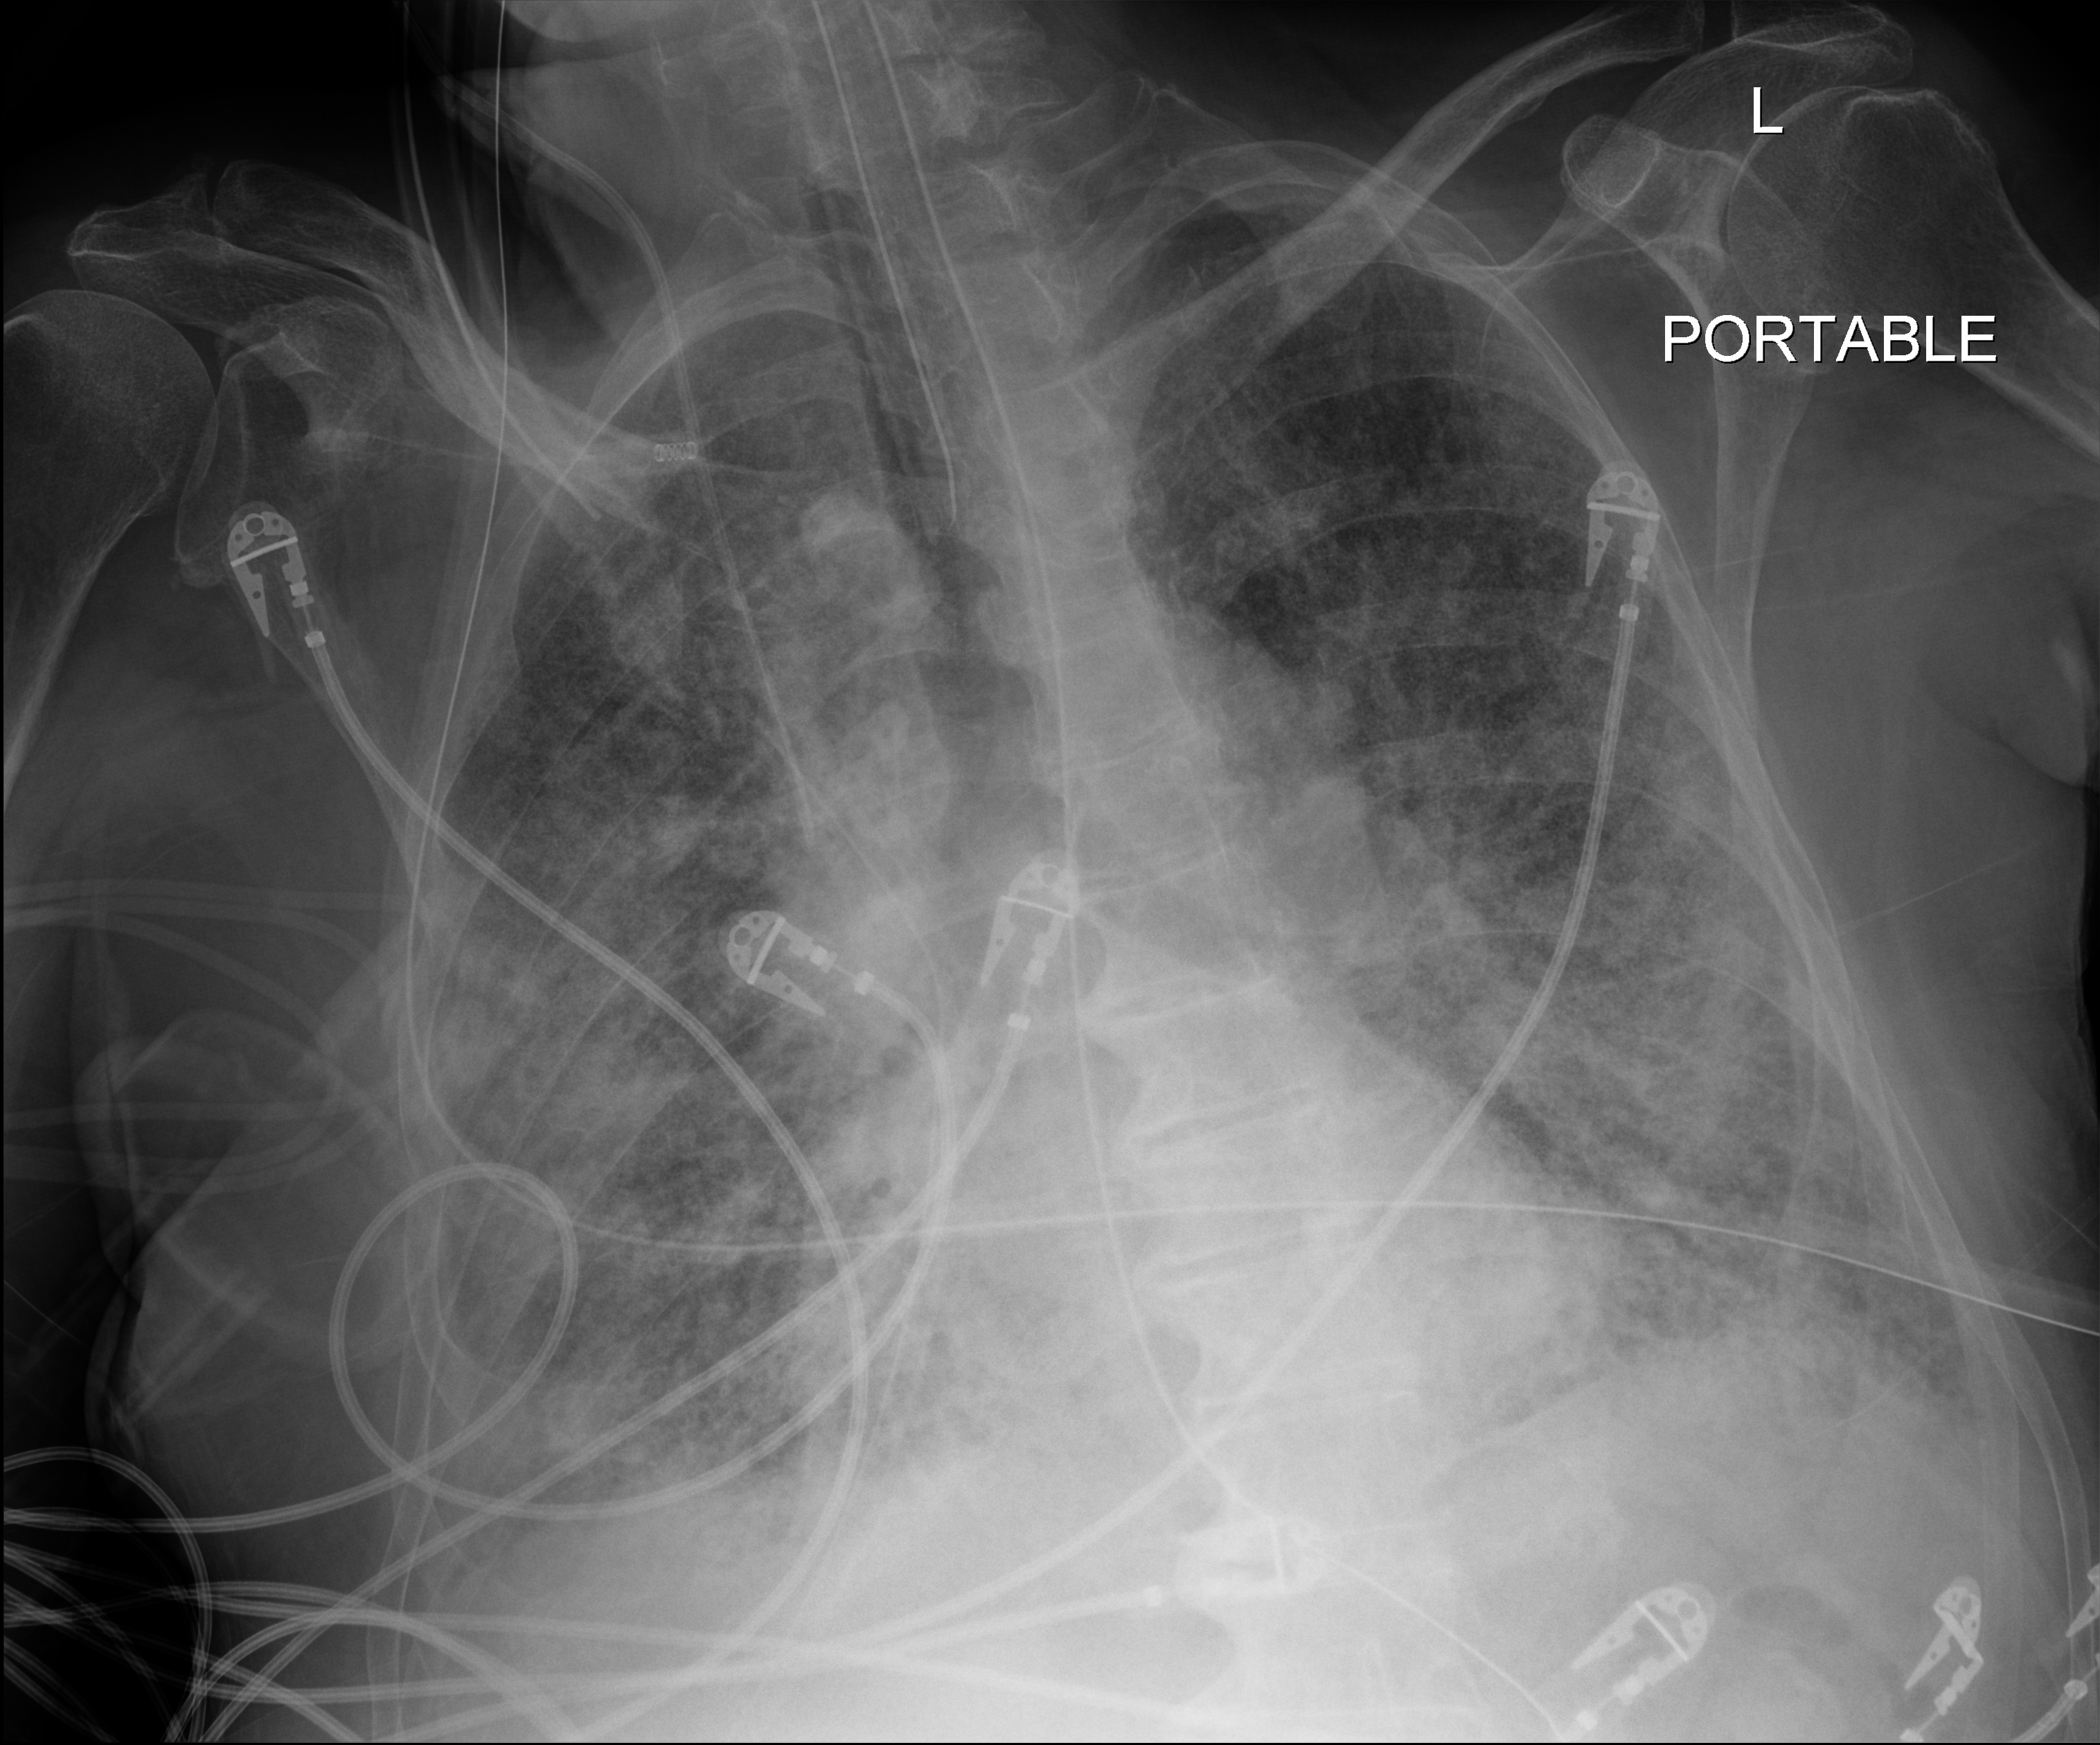
Bedside chest radiograph (digital radiography); anteroposterior (AP) projection. Patient hospitalised with COVID-19; male, aged 75–90 years.
From the hospital-stay record, not from the radiograph (when in the stay this image was taken is not recorded): mechanically ventilated during this hospital stay: yes; length of hospital stay: 47 days; admitted to intensive care during this hospital stay: yes.